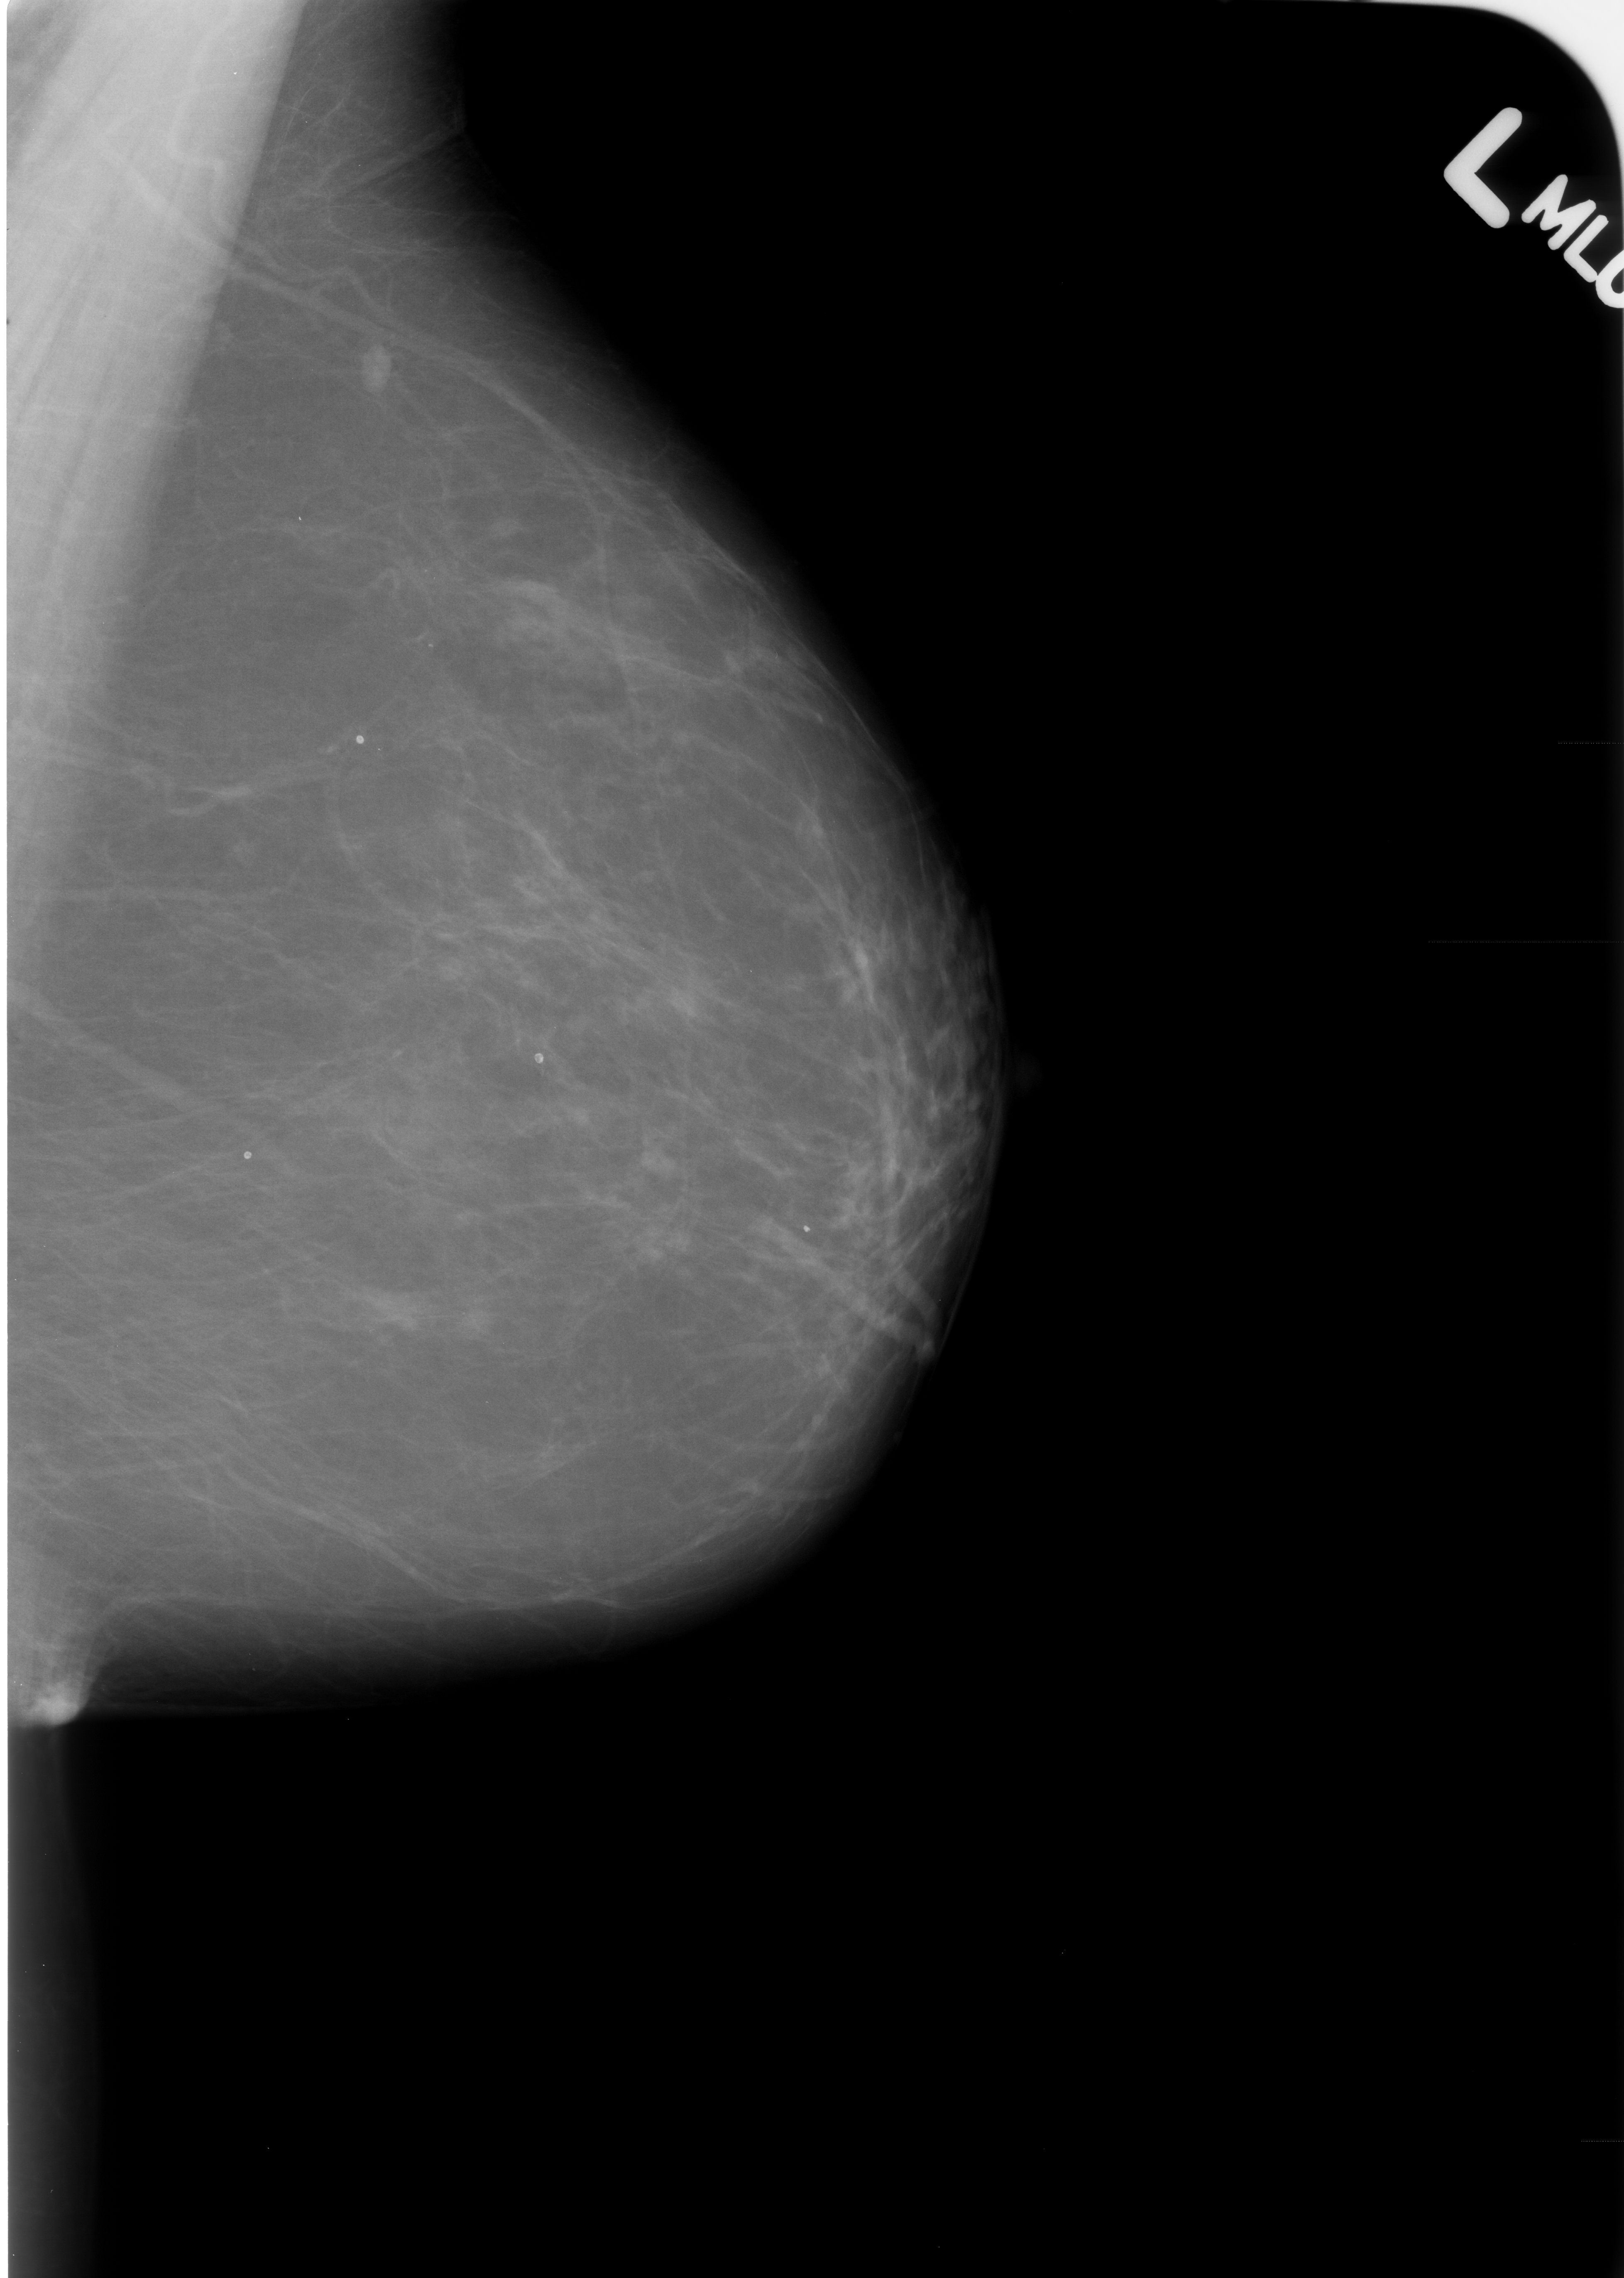
Scanned film-screen mammogram; left breast; MLO view; breast composition: almost entirely fatty (BI-RADS density category 1 of 4); 1624 × 2278 image matrix.
Marked abnormalities (boxes around the expert regions of interest):
- Finding 1 of 4: calcifications, morphology lucent centered; BI-RADS assessment category 2; subtlety rating 3 on a 1 (subtle) to 5 (obvious) scale; benign; no additional work-up was recommended (outcome (as recorded, no biopsy): benign without callback): bounding box [x1, y1, x2, y2] px = [235, 1142, 260, 1173]
- Finding 2 of 4: calcifications, morphology lucent centered; BI-RADS assessment category 2; outcome (as recorded, no biopsy): benign without callback (not worked up further): [338, 720, 373, 758]
- Finding 3 of 4: calcifications, morphology lucent centered; BI-RADS assessment category 2; benign; no additional work-up was recommended (outcome (as recorded, no biopsy): benign without callback): [521, 1036, 559, 1070]
- Finding 4 of 4: calcifications, morphology lucent centered; BI-RADS assessment category 2; outcome (as recorded, no biopsy): benign without callback (not worked up further): [793, 1208, 825, 1246]